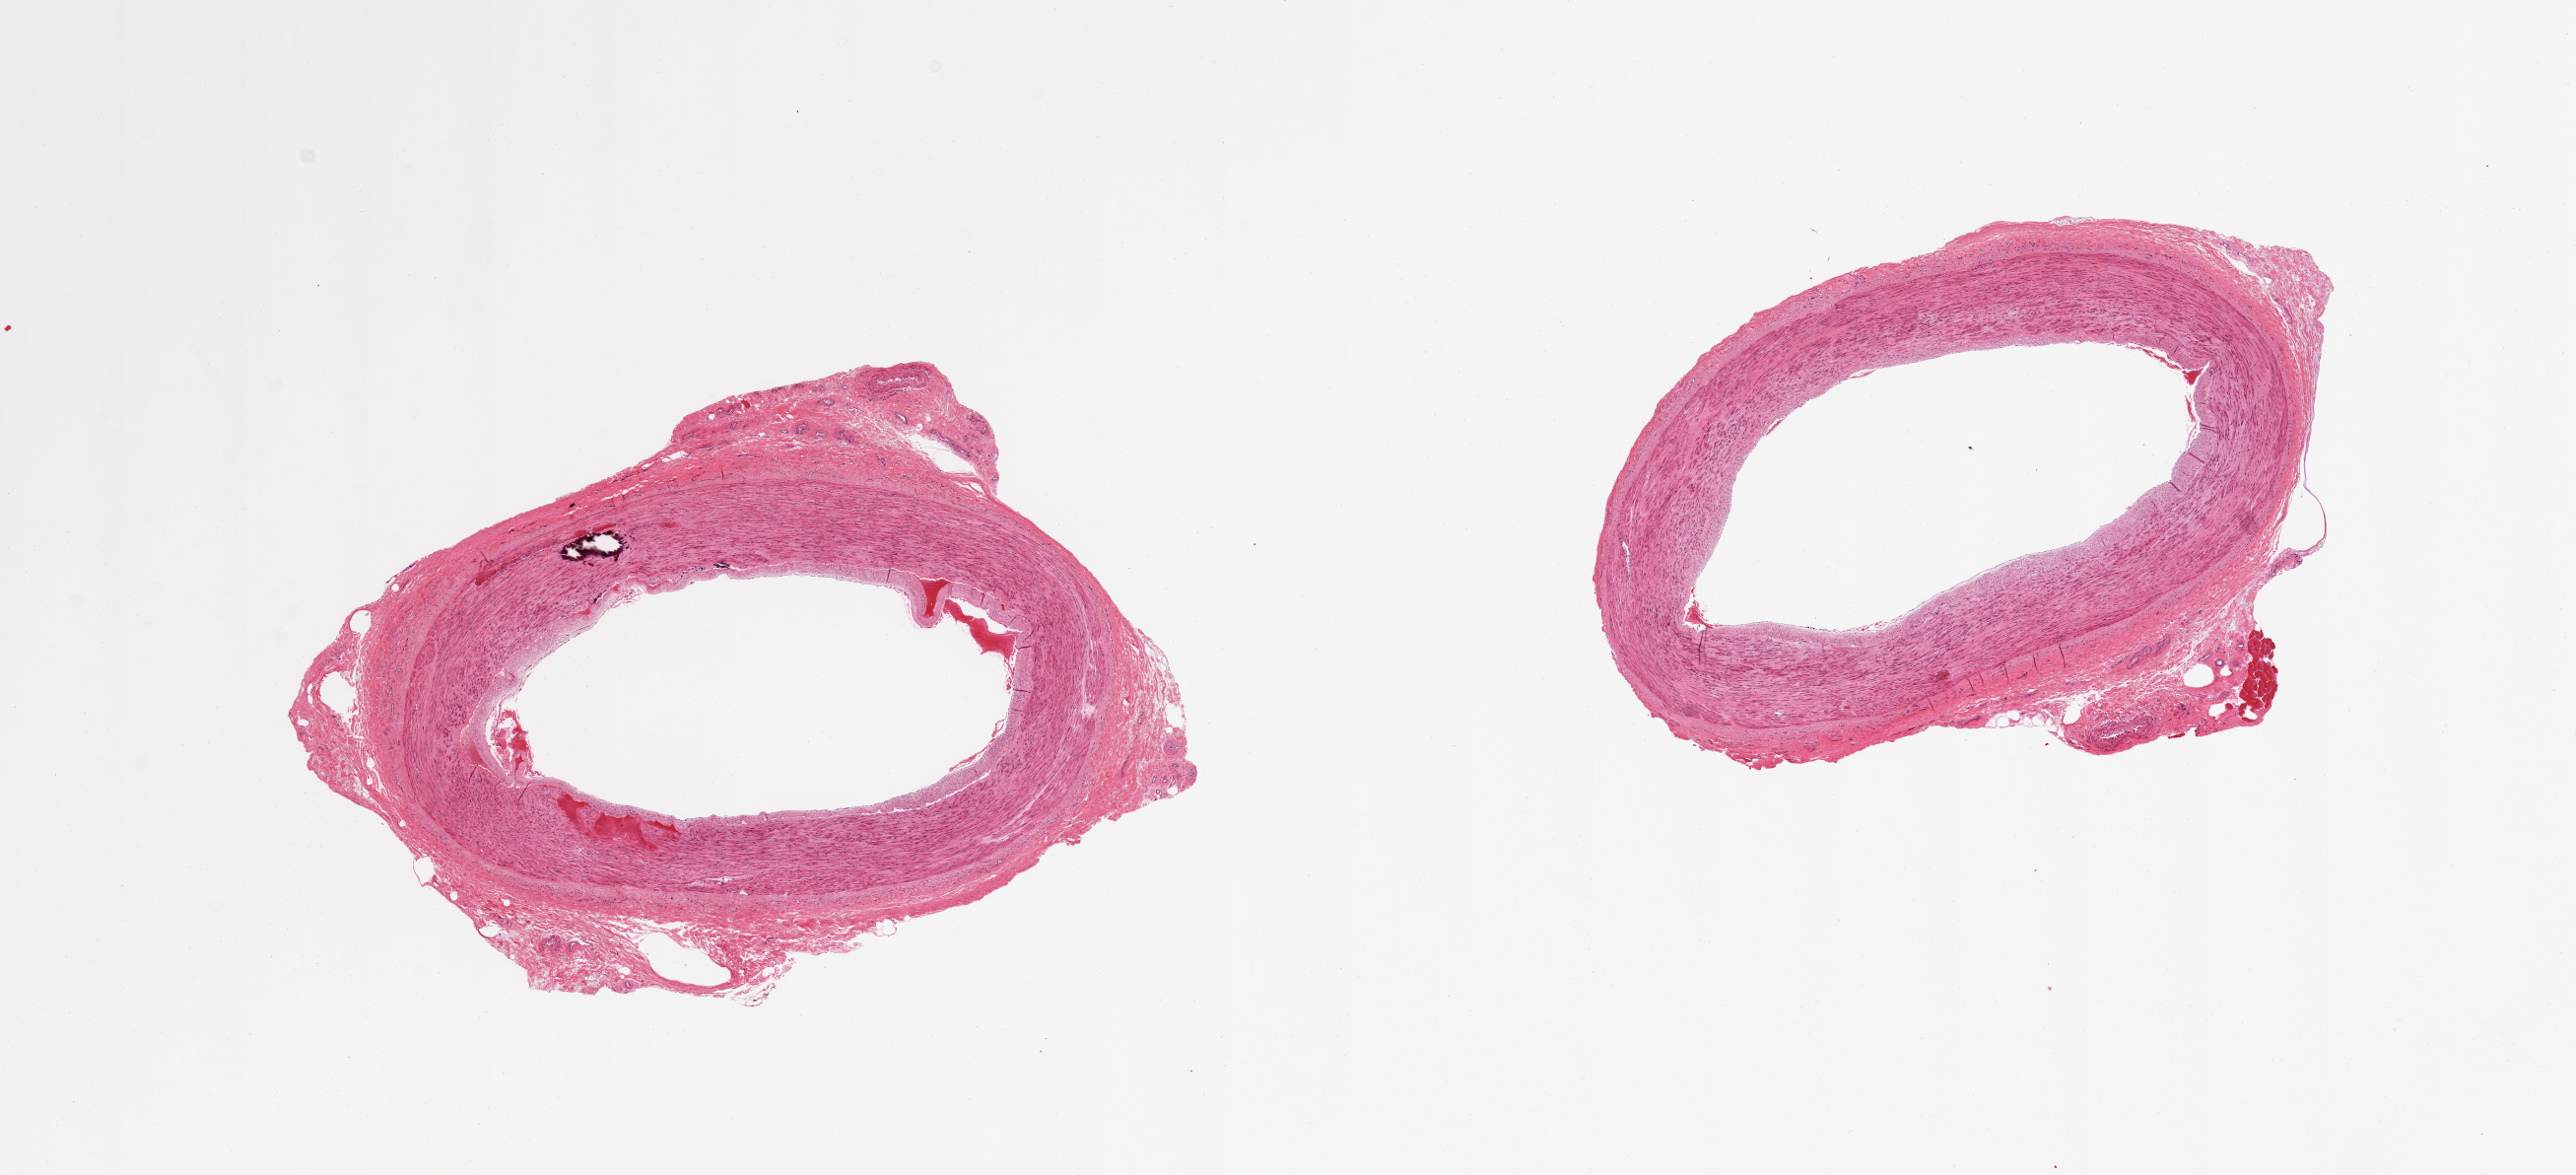
Whole-slide image, haematoxylin and eosin stain, brightfield — a low-resolution overview of the entire scanned area, about 20.7 x 9.4 mm; PAXgene-fixed paraffin-embedded (PFPE) section; section of tibial artery (target tissue); tissue donor sample. Male donor.
* pathologist's review note for this sample: 2 pieces, medial calcific sclerosis